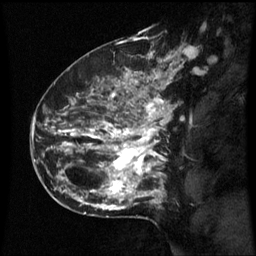
Breast MRI (dynamic contrast-enhanced), one sagittal slice; position 41 of 60 along the scan axis; dynamic contrast-enhanced series, image 2 of 3 at this slice position (ordered by acquisition); 1.5 T; TE 4.2 ms, TR 8.9 ms; 2.1 mm slice thickness; 256 × 256 image matrix, field of view 200 × 200 mm. Female patient, age 42 years. Case-level facts recorded for this patient, not image findings: setting: breast cancer imaged before/during neoadjuvant chemotherapy; receptor status: HER2-positive.
Annotated regions visible in this slice (semi-automatically segmented with operator editing):
- analysis volume of interest (the breast-tissue region the enhancement analysis was run in; not a lesion): bounding box (x1, y1, x2, y2) in pixels: (66, 82, 173, 193)
- tumour enhancement mask (voxels above the 70 % enhancement threshold inside the analysis volume of interest): (66, 82, 171, 193)